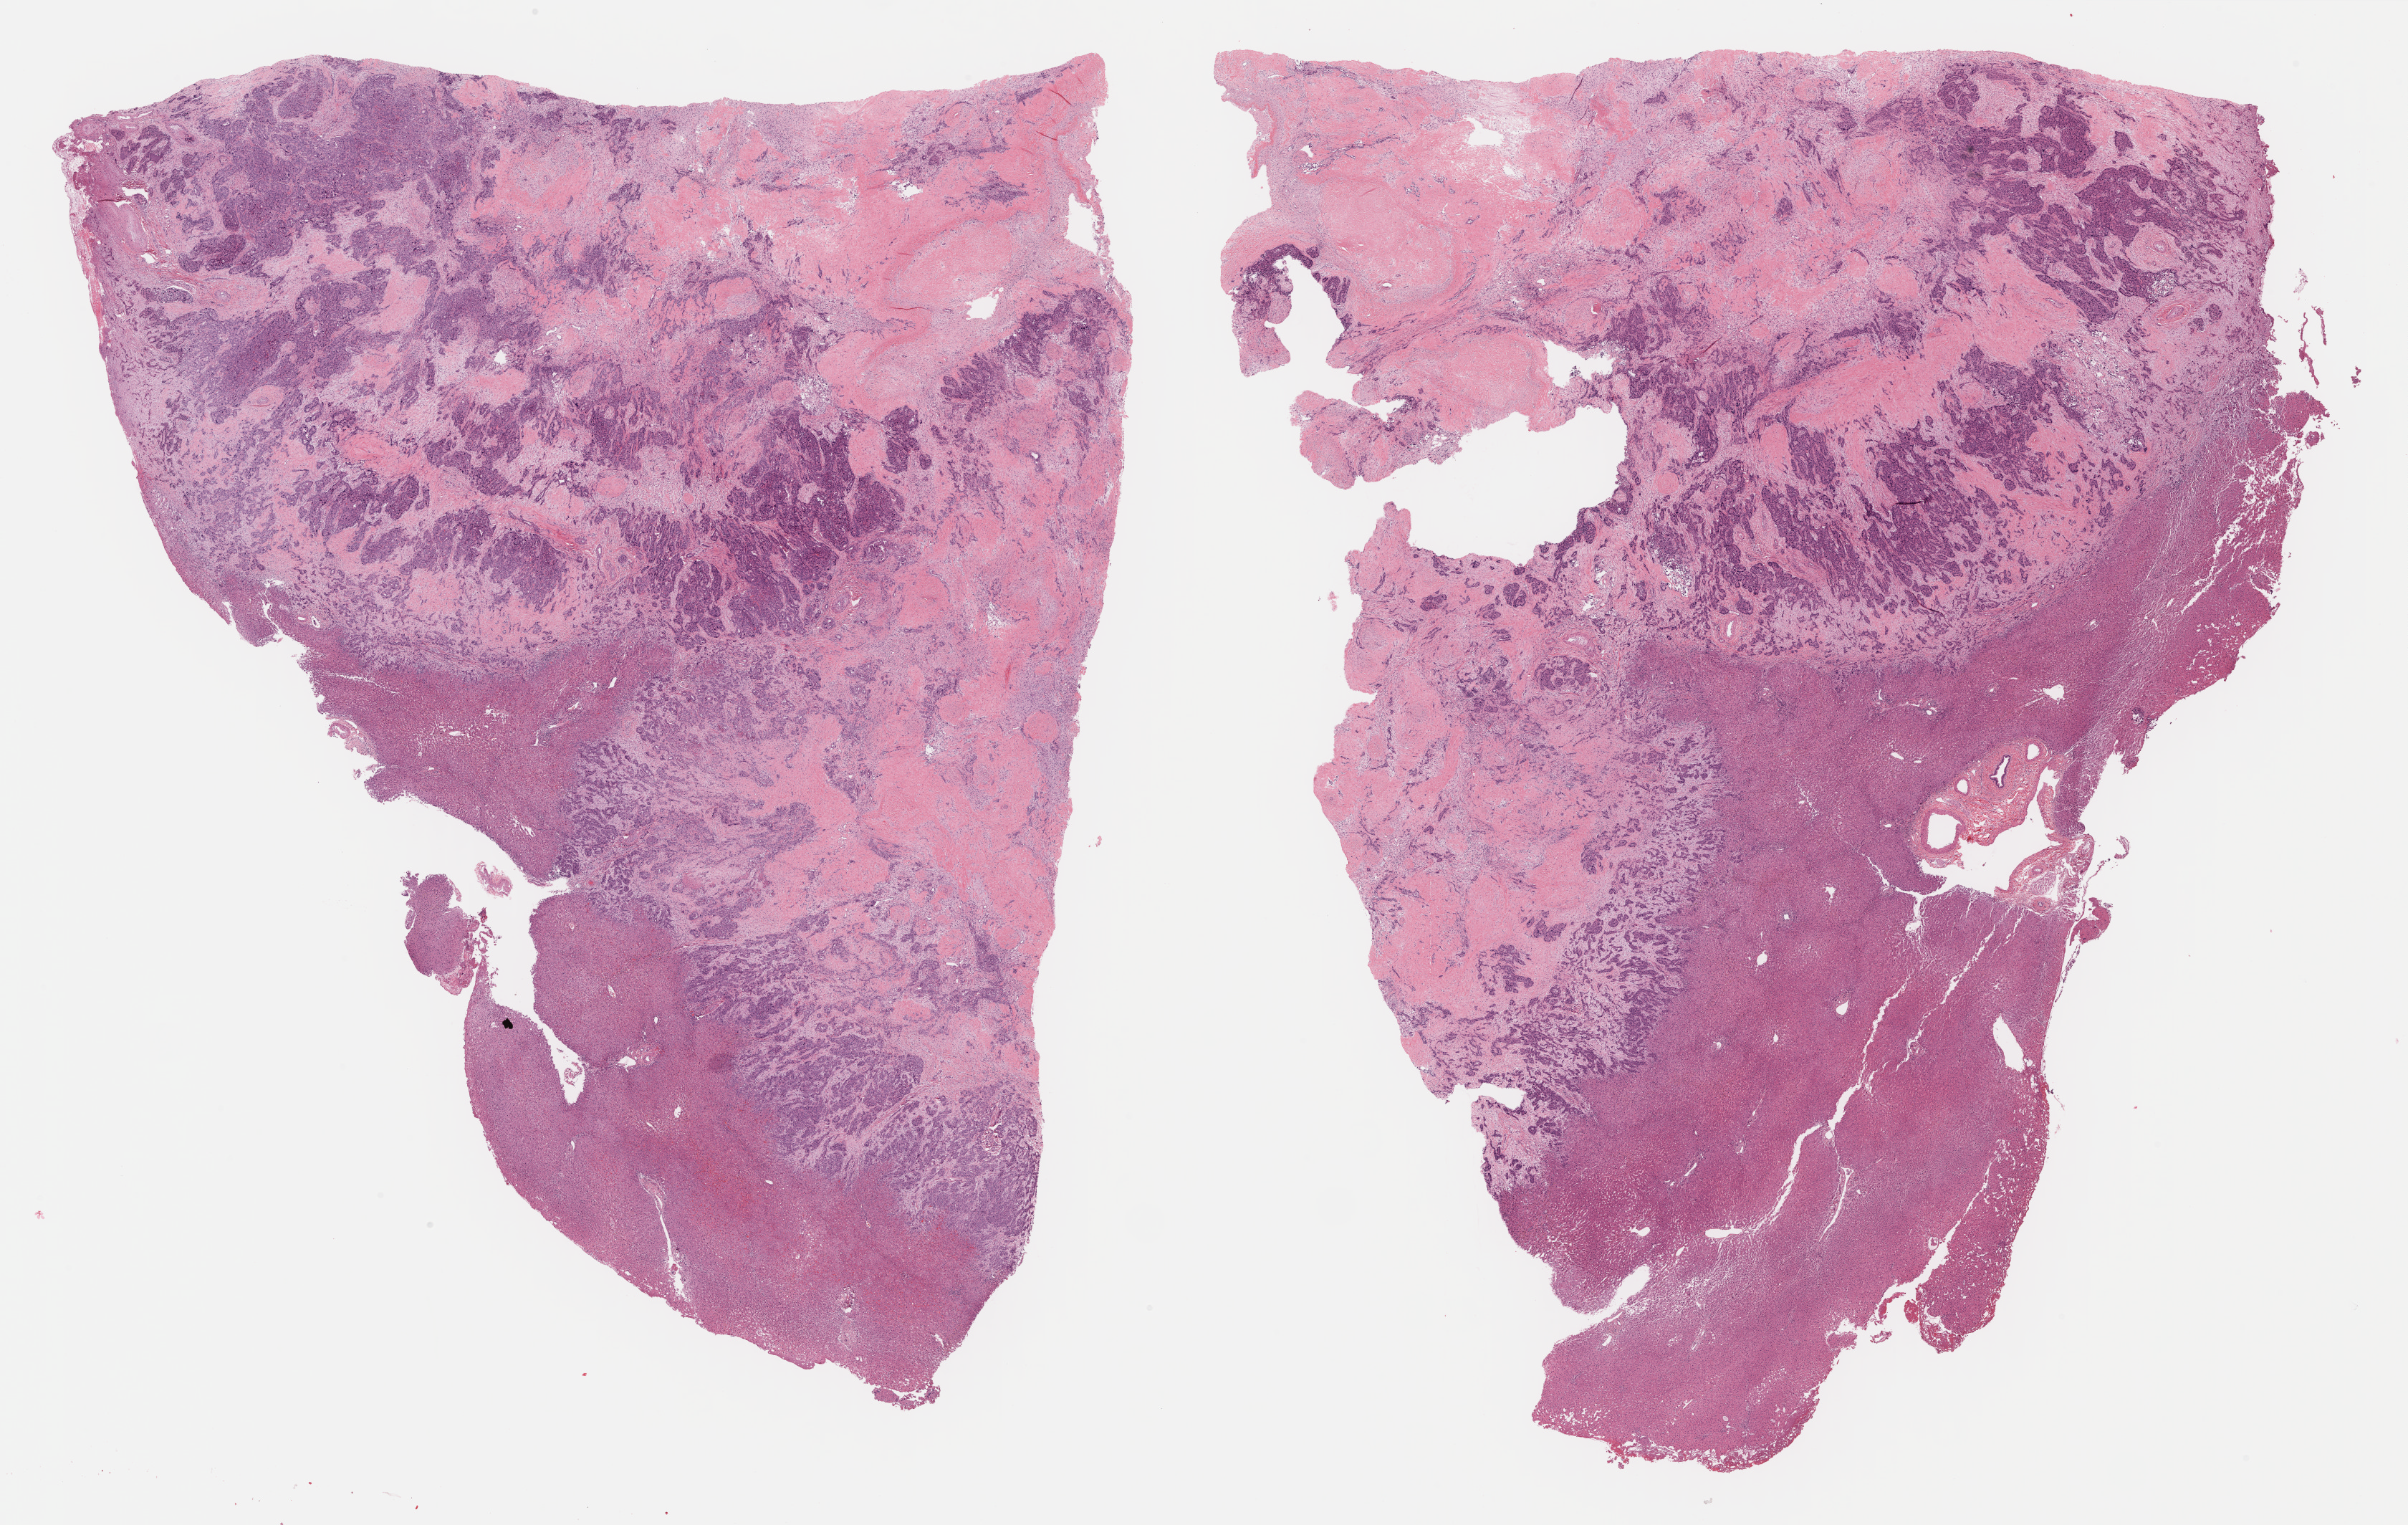
Whole-slide histology image, Hematoxylin and eosin (H&E) stained, a low-resolution overview of the entire scanned area, about 27.2 x 17.2 mm (acquisition: 40x scan), formalin-fixed paraffin-embedded (FFPE) diagnostic section, sample: primary tumour, bile duct. Patient: female, age at initial diagnosis 51 years. Histologic grade: G3 (poorly differentiated).
AJCC pathologic stage: IV (6th edition). Pathologic diagnosis: Cholangiocarcinoma (intrahepatic bile duct). TNM: T3 N0 M1.